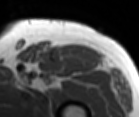
MRI of an extremity soft-tissue mass, one axial slice; position 78 of 86 along the scan axis; MR volume resampled by the dataset authors to the PET/CT grid (not the native acquisition matrix); 3.27 mm slice thickness; 139 × 117 image matrix. Male patient. From the clinical record (not read from this slice): histological type: extraskeletal osteosarcoma; grade: high; site of the primary tumour: thigh.
Annotated regions visible in this slice (expert contour drawn on MRI and transferred to this co-registered scan by the dataset authors):
- gross tumour volume (mass): bounding box (x1, y1, x2, y2) in pixels: (61, 43, 101, 65)